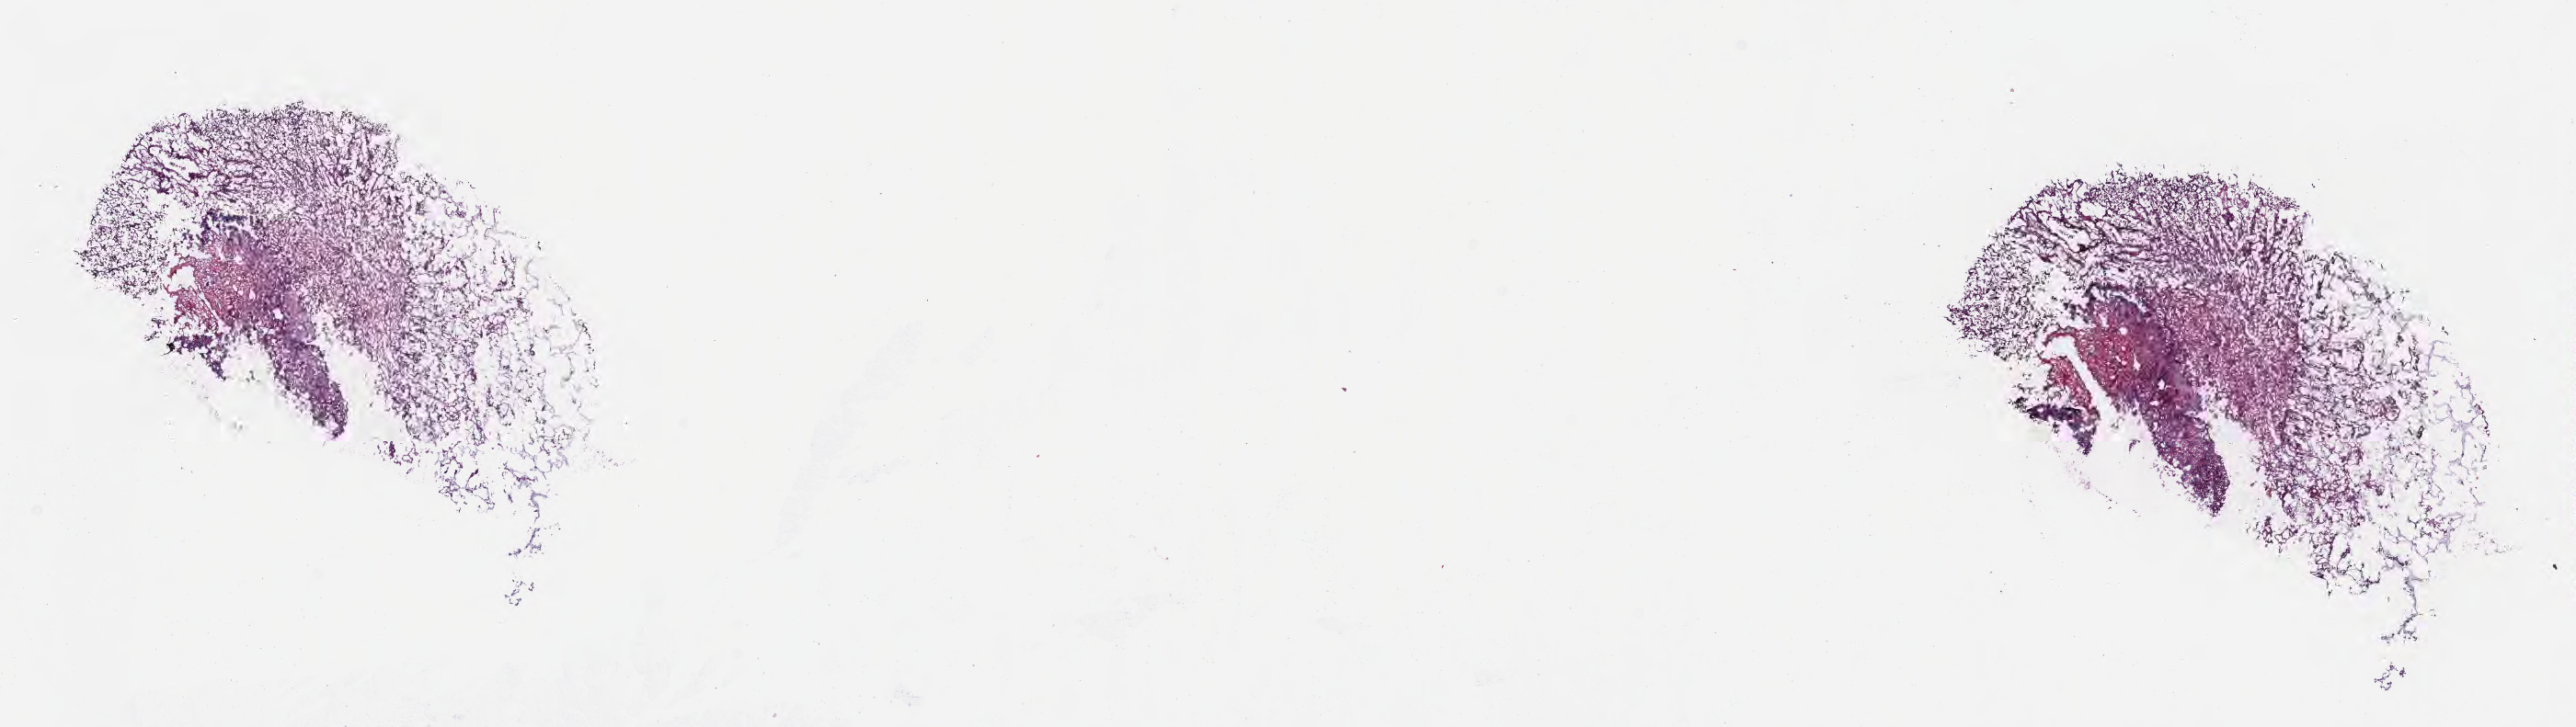
Whole-slide image, haematoxylin and eosin stain, a low-resolution overview of the entire scanned area, about 22.6 x 6.4 mm; frozen section; primary tumor; site: sigmoid colon. Patient sex: female. Tumor grade: G4 (undifferentiated). Composition of this section per pathologist review: tumor cells 75%, tumor nuclei 75%, stromal cells 22%, necrosis 0%, normal cells 3%. Infiltration values recorded for this section: lymphocyte infiltration 4%, monocyte infiltration 3%, neutrophil infiltration 7%.
Section: top of the tissue portion. Diagnosis: Adenocarcinoma, NOS.